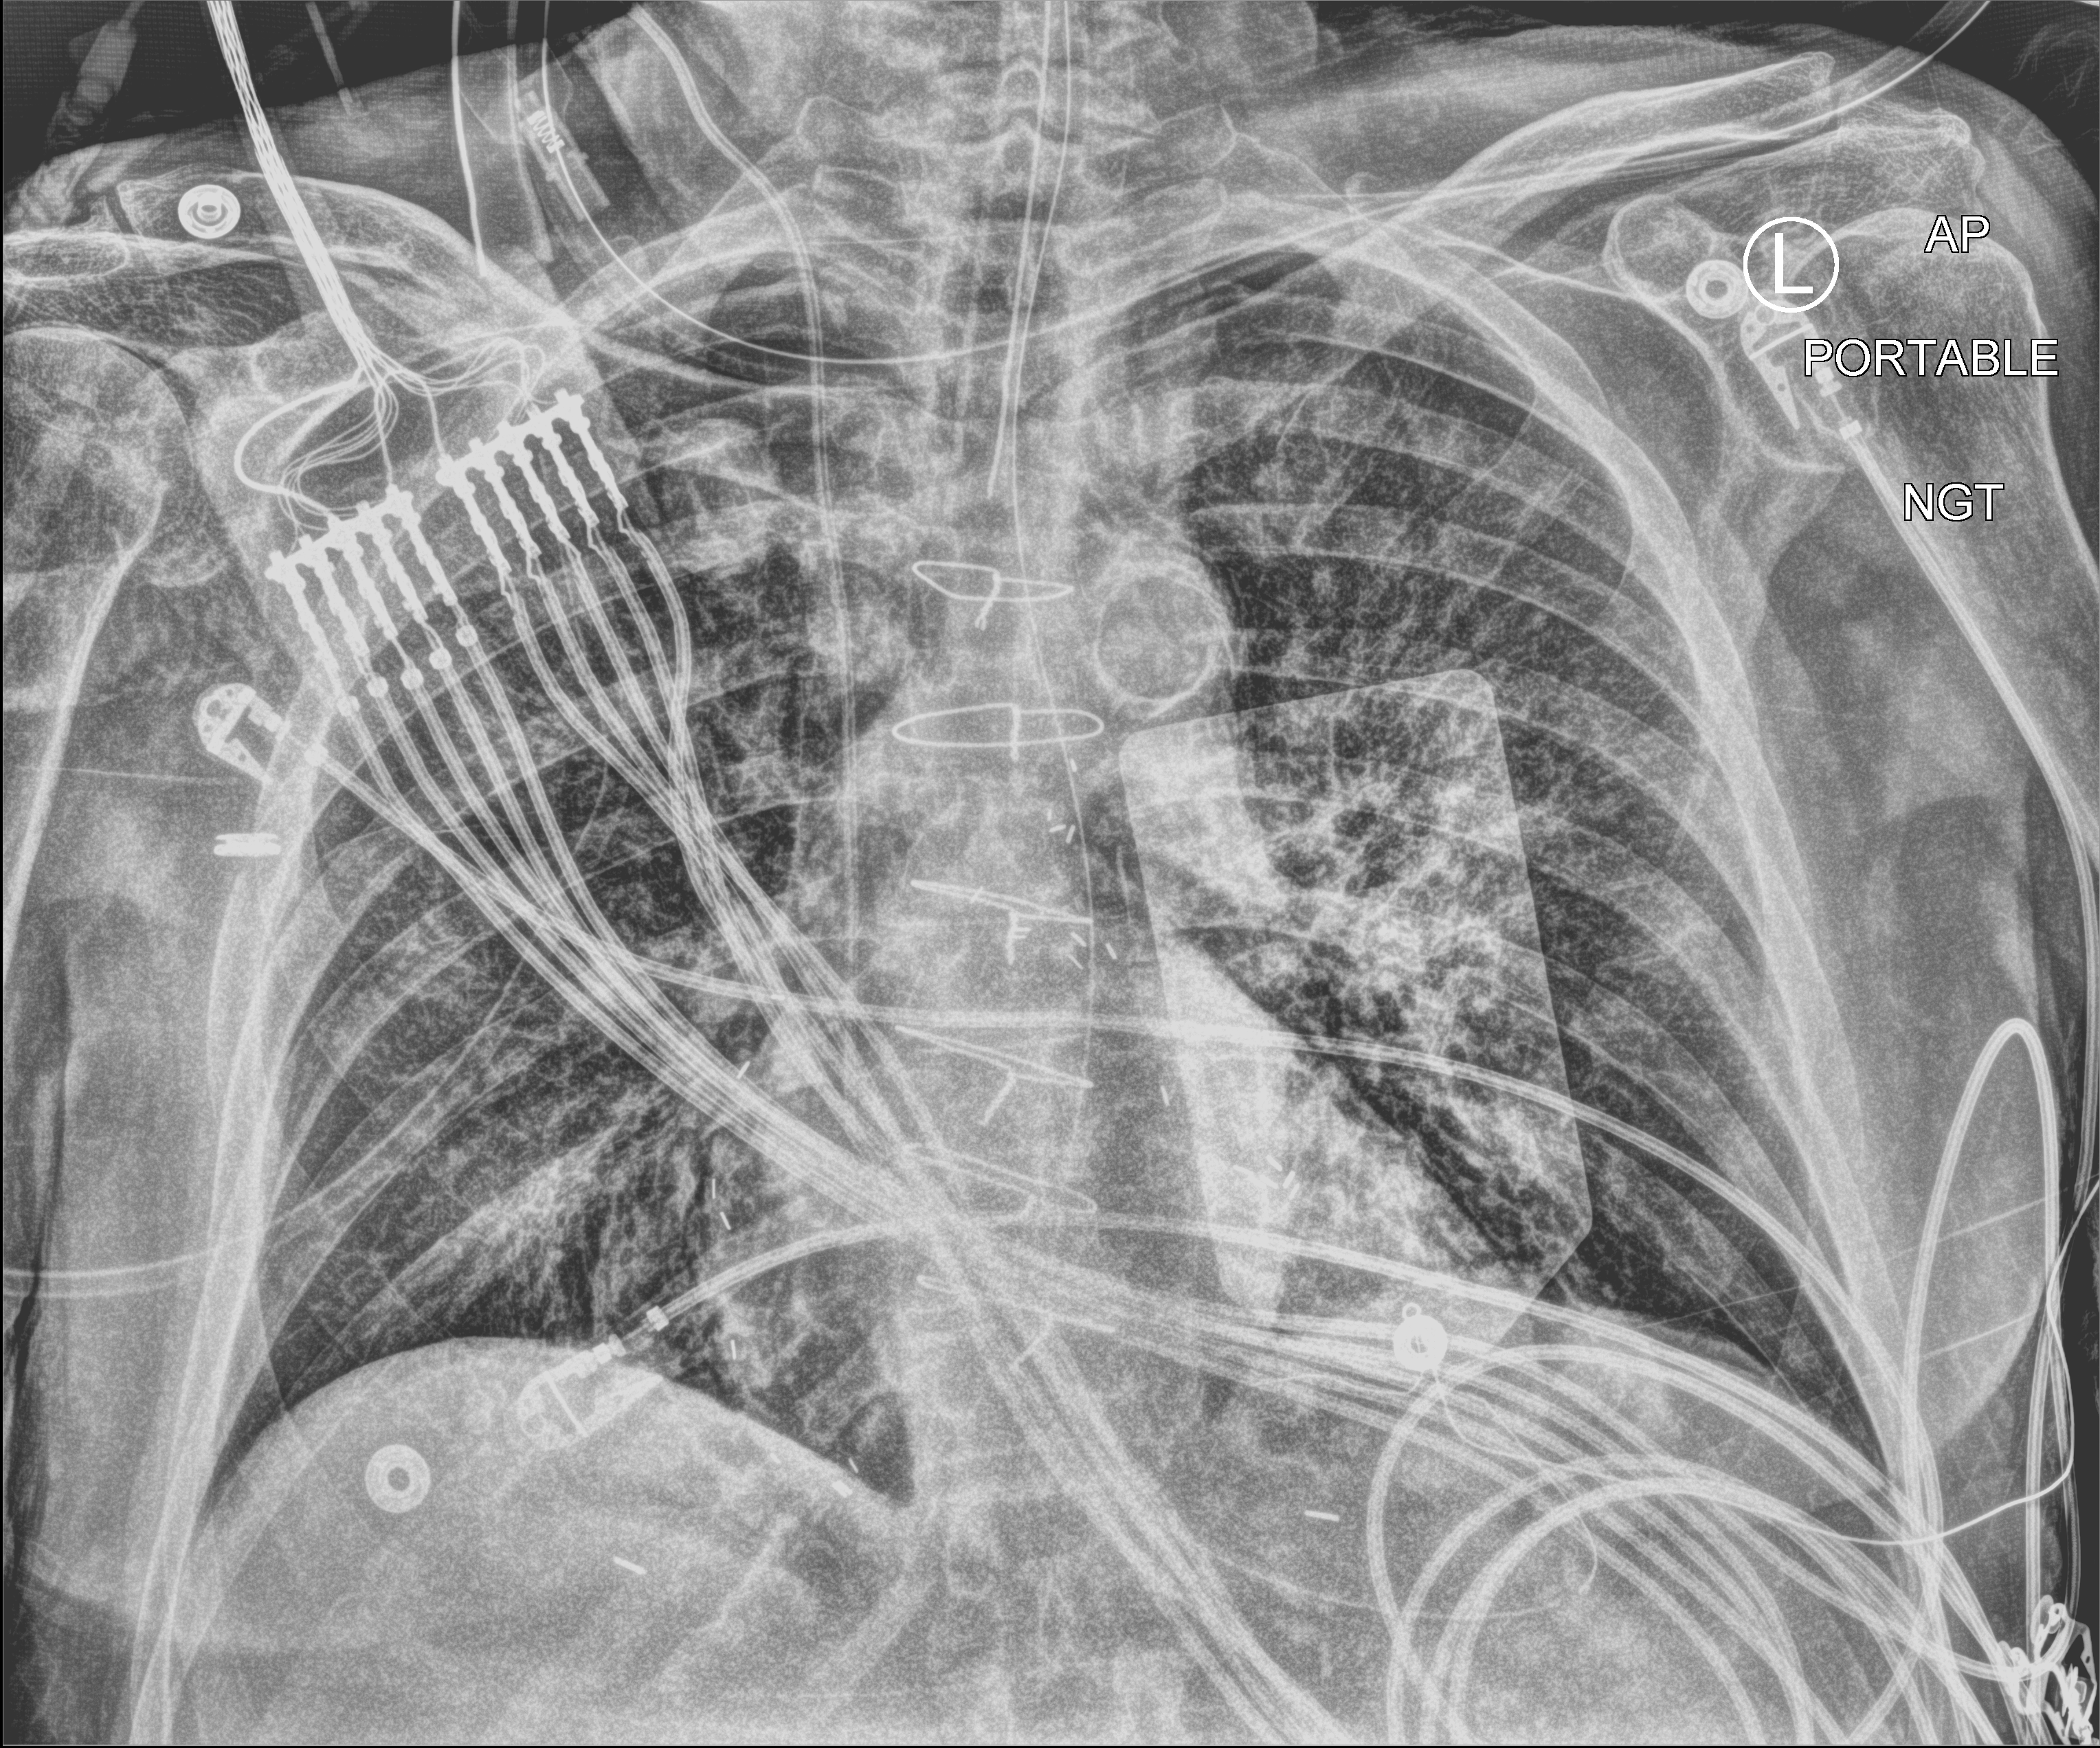
Portable chest radiograph. Patient hospitalised with COVID-19; male, aged 75–90 years.
Hospital-stay facts (about this admission, not read from this image; timing relative to this image not recorded):
- mechanically ventilated during this hospital stay: yes
- other chronic lung disease (admission record): no
- hypertension (admission record): yes